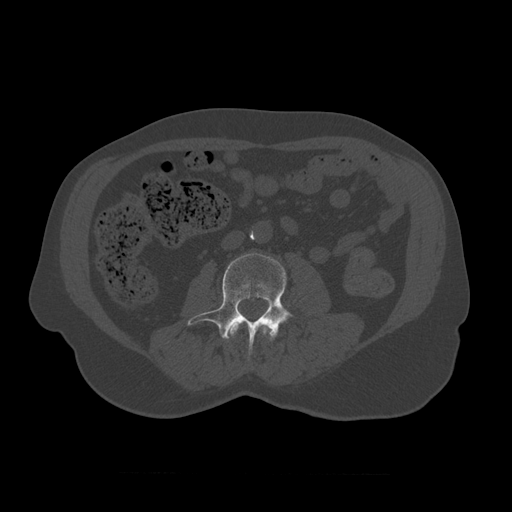
CT including the spine, one axial slice; slice 305 of 450 in the series (ordered by position); reconstruction kernel STANDARD; 120 kVp; bone window (W 1800 / L 400 HU); 1.25 mm slice thickness; 512 × 512 image matrix, field of view 405 × 405 mm. Patient age 75 years. Case-level facts recorded for this patient, not image findings: primary cancer: prostate.
Structures marked on this image (semi-automatically segmented with operator editing):
- L2 vertebra: box from (x=230, y=321) to (x=271, y=338) px
- L3 vertebra: (x=187, y=253)–(x=294, y=356)